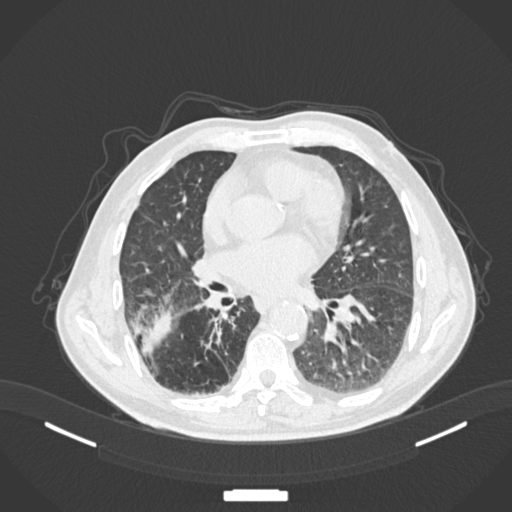
Chest CT, one axial slice. Slice 72 of 201 in the series (ordered by position). 120 kVp. Lung window (W 1500 / L -600 HU). 1 mm slice thickness. 512 × 512 image matrix, field of view 400 × 400 mm. Patient: male, 72 years. From the clinical record (not read from this slice): clinical TNM (as recorded): T3 N2 M0.
Annotated regions visible in this slice (bounding box drawn by a radiologist):
- lung tumour (recorded histology: adenocarcinoma): bounding box <133,311,174,354> (left, top, right, bottom; pixels)